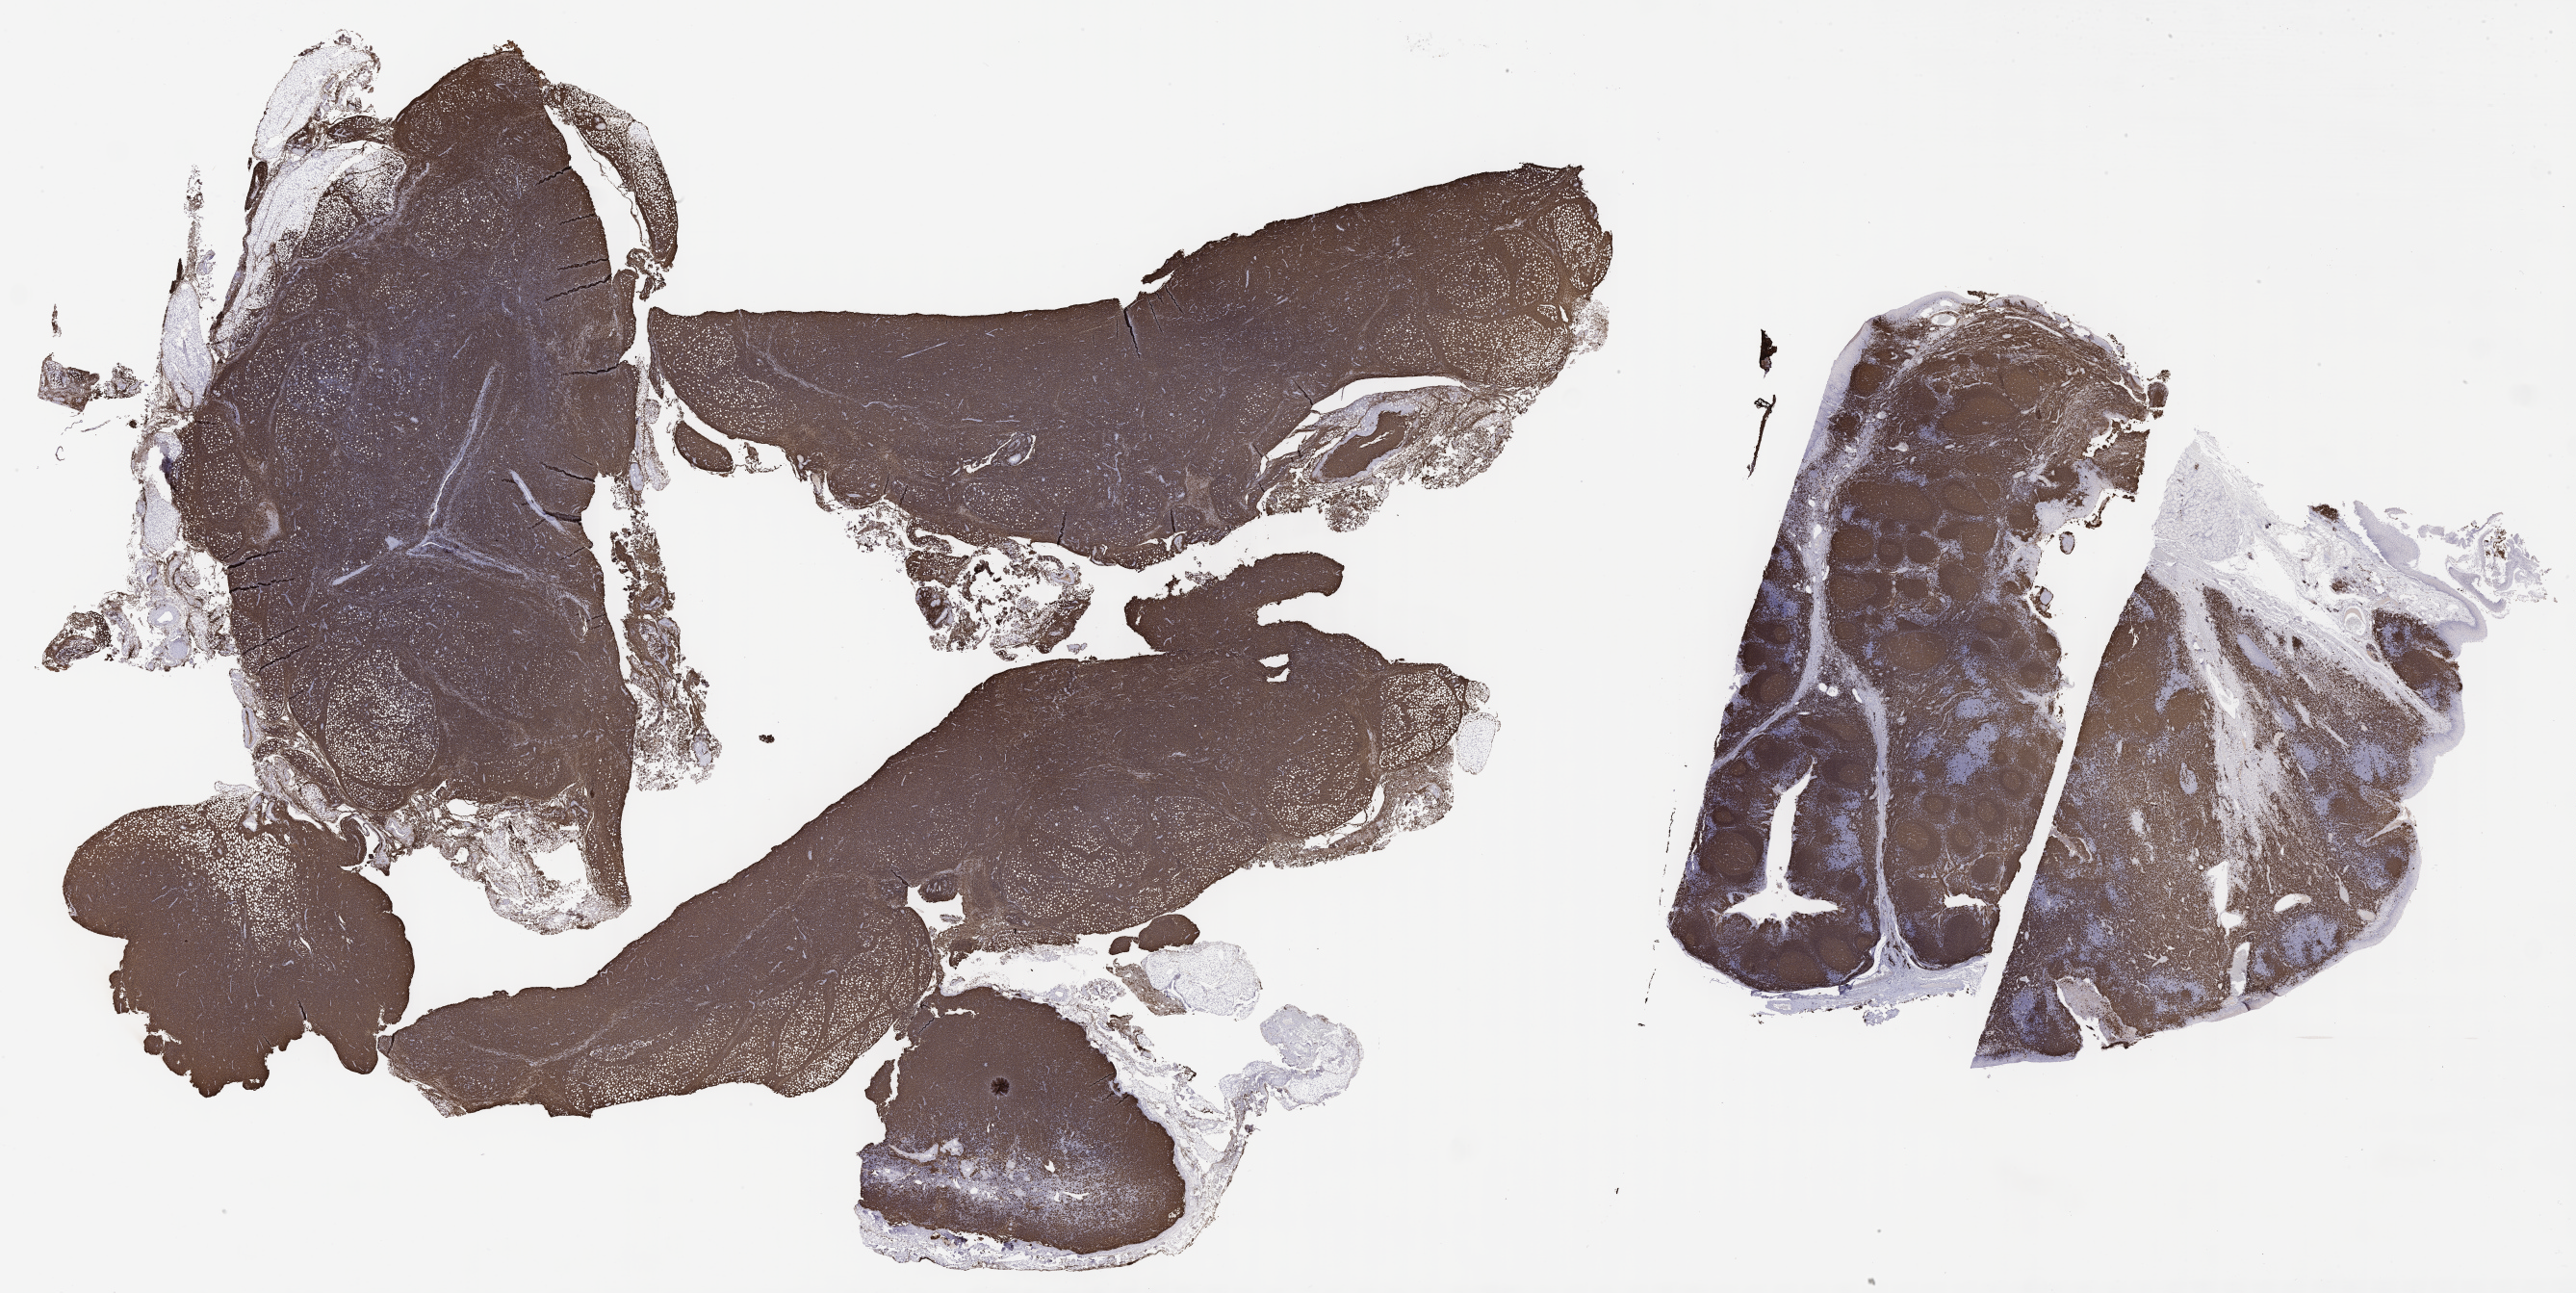
IHC for CD20, whole-slide image, a low-resolution overview of the entire scanned area, about 43.3 x 21.7 mm; tumor tissue; anatomic site: lymph node. Patient: male, aged 68.
Histologic diagnosis: Diffuse large B-cell lymphoma, NOS.